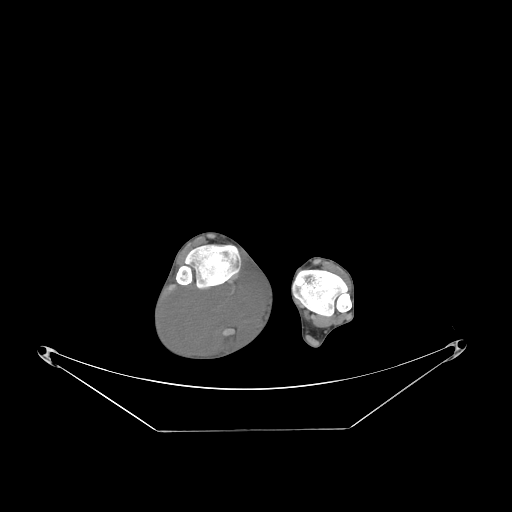
CT of an extremity soft-tissue mass (from a PET/CT study), one axial slice; slice 50 of 267 in the series (ordered by position); reconstruction kernel STANDARD; soft-tissue window (W 400 / L 40 HU); 3.75 mm slice thickness; 512 × 512 image matrix. Male patient. Case-level facts recorded for this patient, not image findings: histological type: liposarcoma - round cell; grade: high; site of the primary tumour: right calf.
Annotated regions visible in this slice (expert contour drawn on MRI and transferred to this co-registered scan by the dataset authors):
- gross tumour volume (mass): bounding box [x1, y1, x2, y2] px = [164, 274, 266, 357]